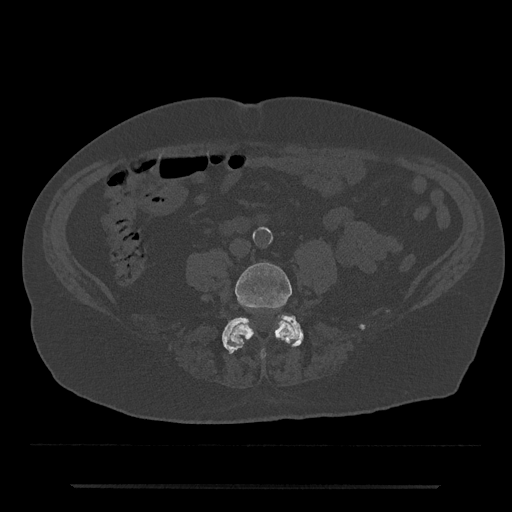
CT including the spine, one axial slice. Slice 328 of 797 in the series (ordered by position). Reconstruction kernel Br40s/3. 120 kVp. Bone window (W 1800 / L 400 HU). 512 × 512 image matrix. Patient: male, 80 years. Case-level facts recorded for this patient, not image findings: primary cancer: prostate; vertebrae with lytic lesions (as recorded): L1, T11.
Outlined on this slice (semi-automatic segmentation, software-assisted and operator-edited):
- L4 vertebra: bounding box <228,262,297,358> (left, top, right, bottom; pixels)
- L5 vertebra: <222,315,303,354>